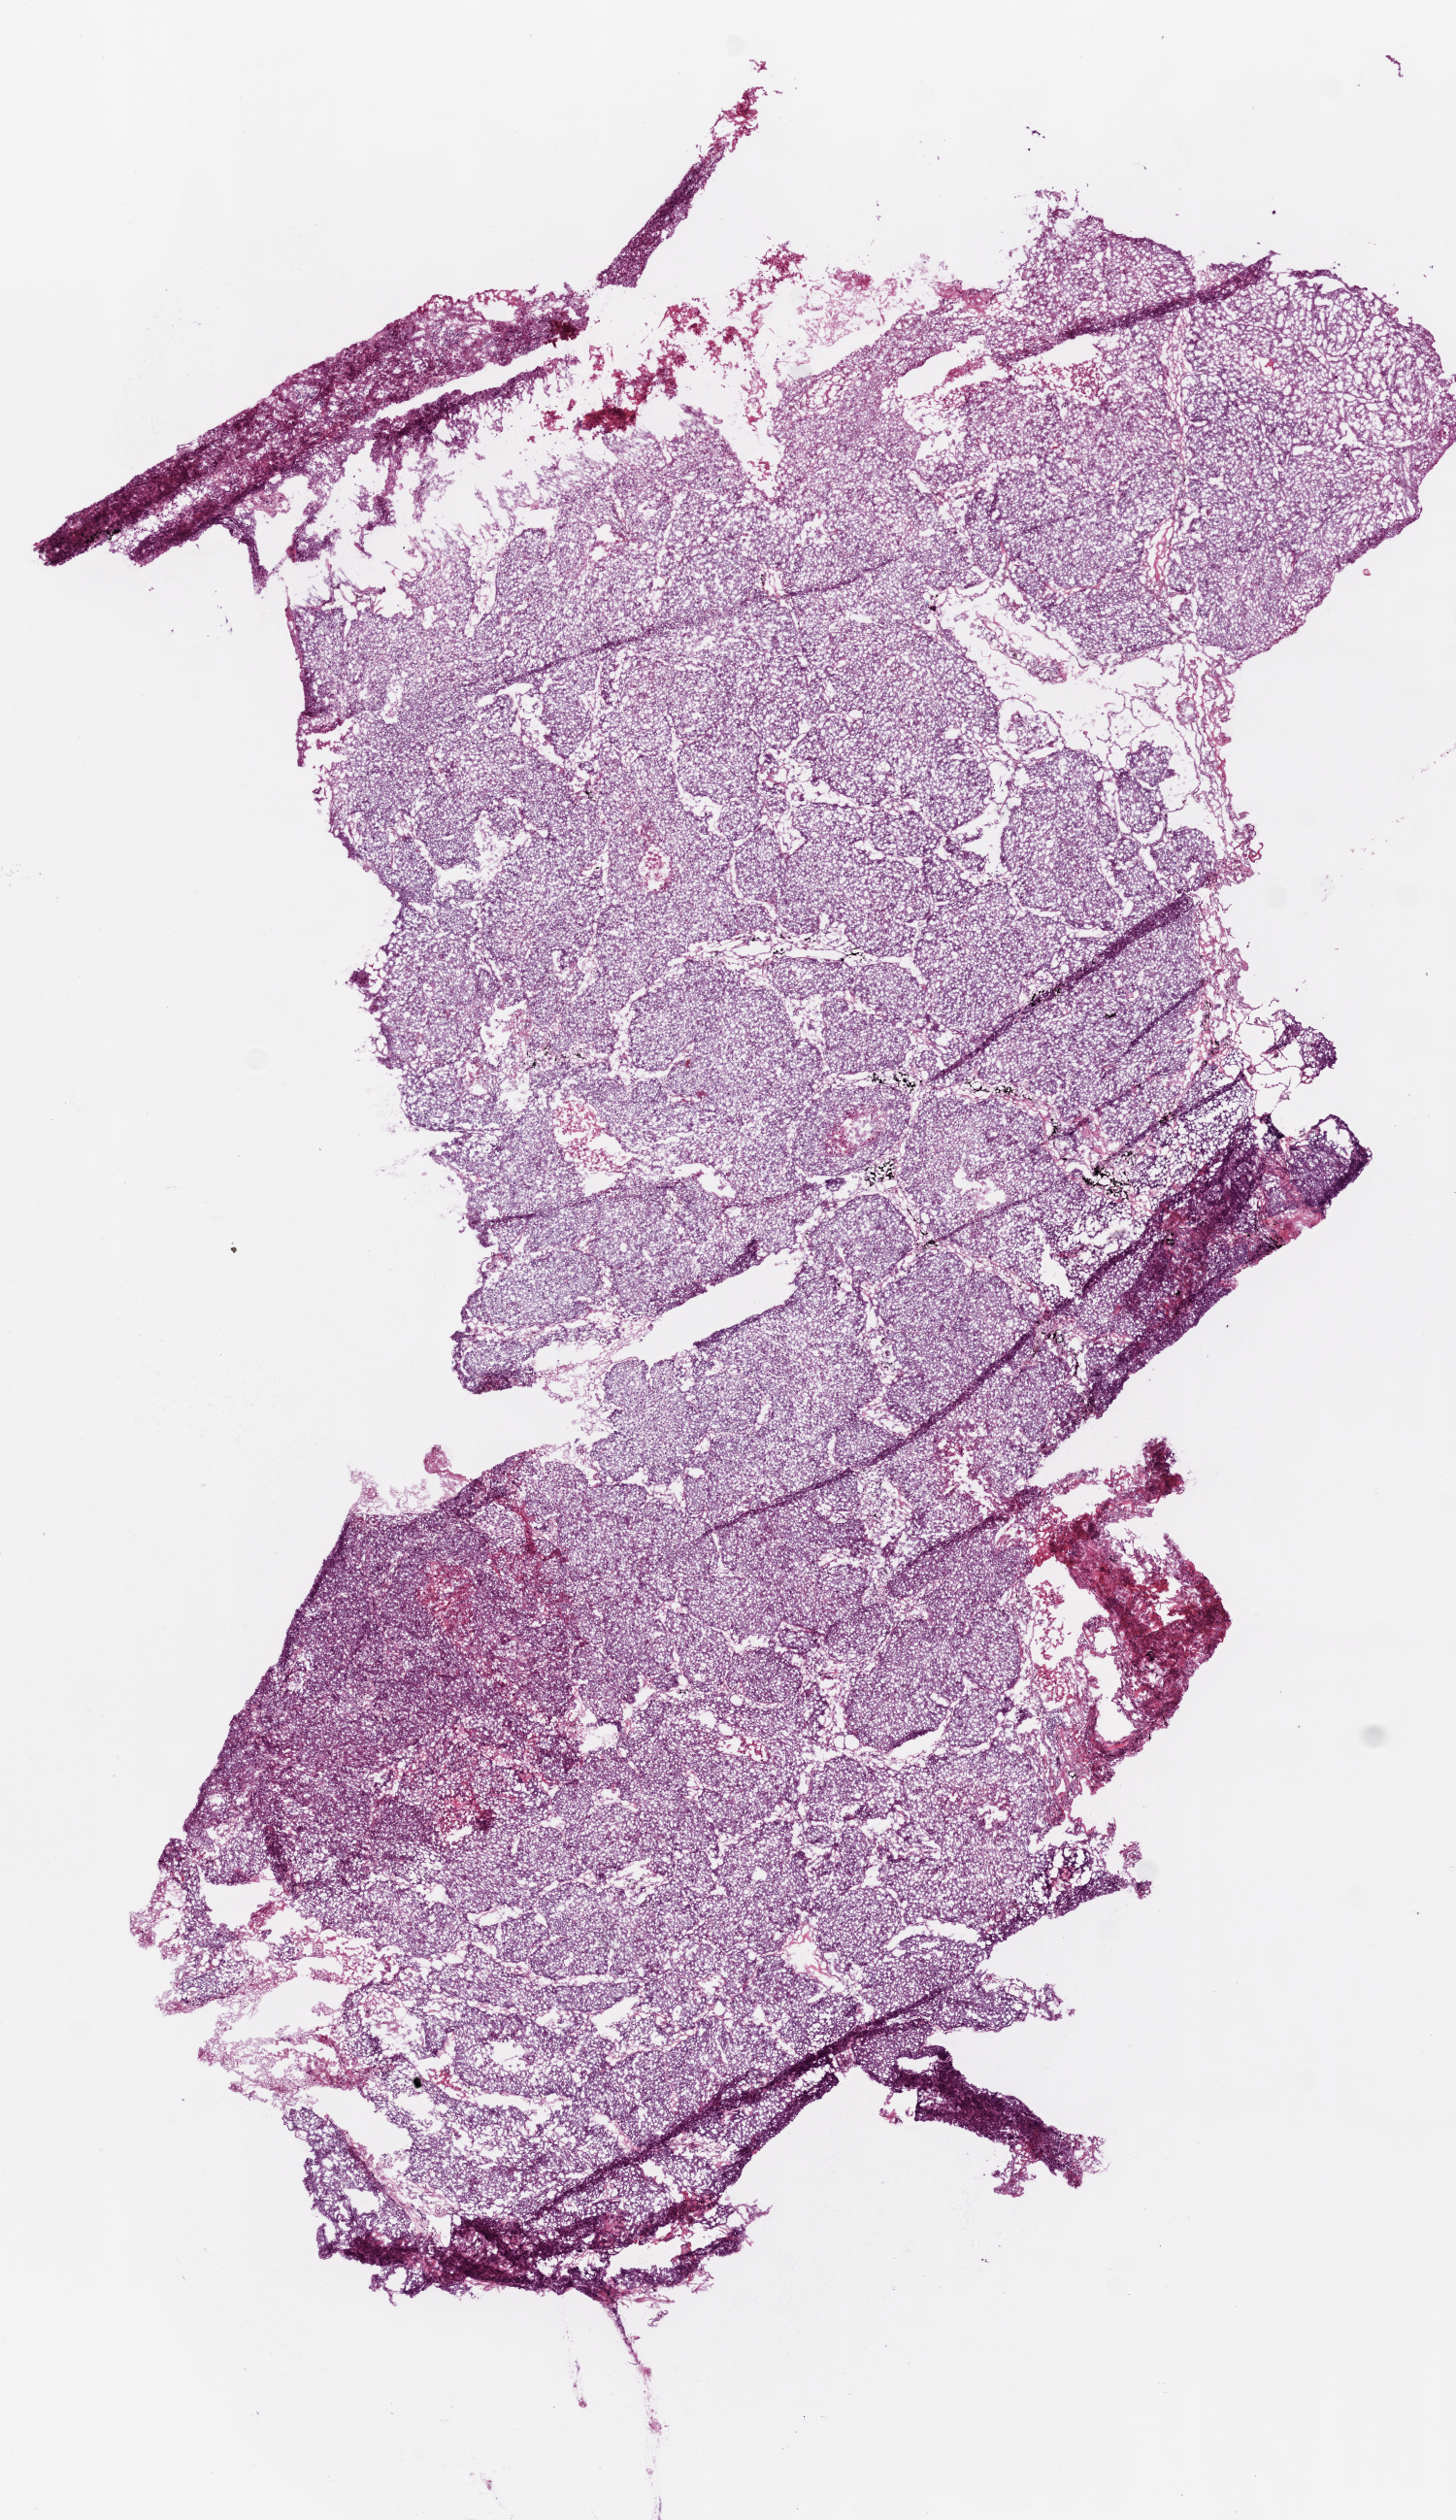
Hematoxylin and eosin (H&E) stained whole-slide image, a low-resolution overview of the entire scanned area, about 6.0 x 10.4 mm (from a 20x scan), frozen section, lung, primary tumour sample. Patient: female, age at initial diagnosis 76 years. Composition of this section per pathologist review: tumour cells 85%, tumour nuclei 90%, normal cells 0%, stromal cells 10%, necrosis 5%.
AJCC pathologic stage: IA. Histologic diagnosis: Squamous cell carcinoma, NOS (lower lobe, lung).